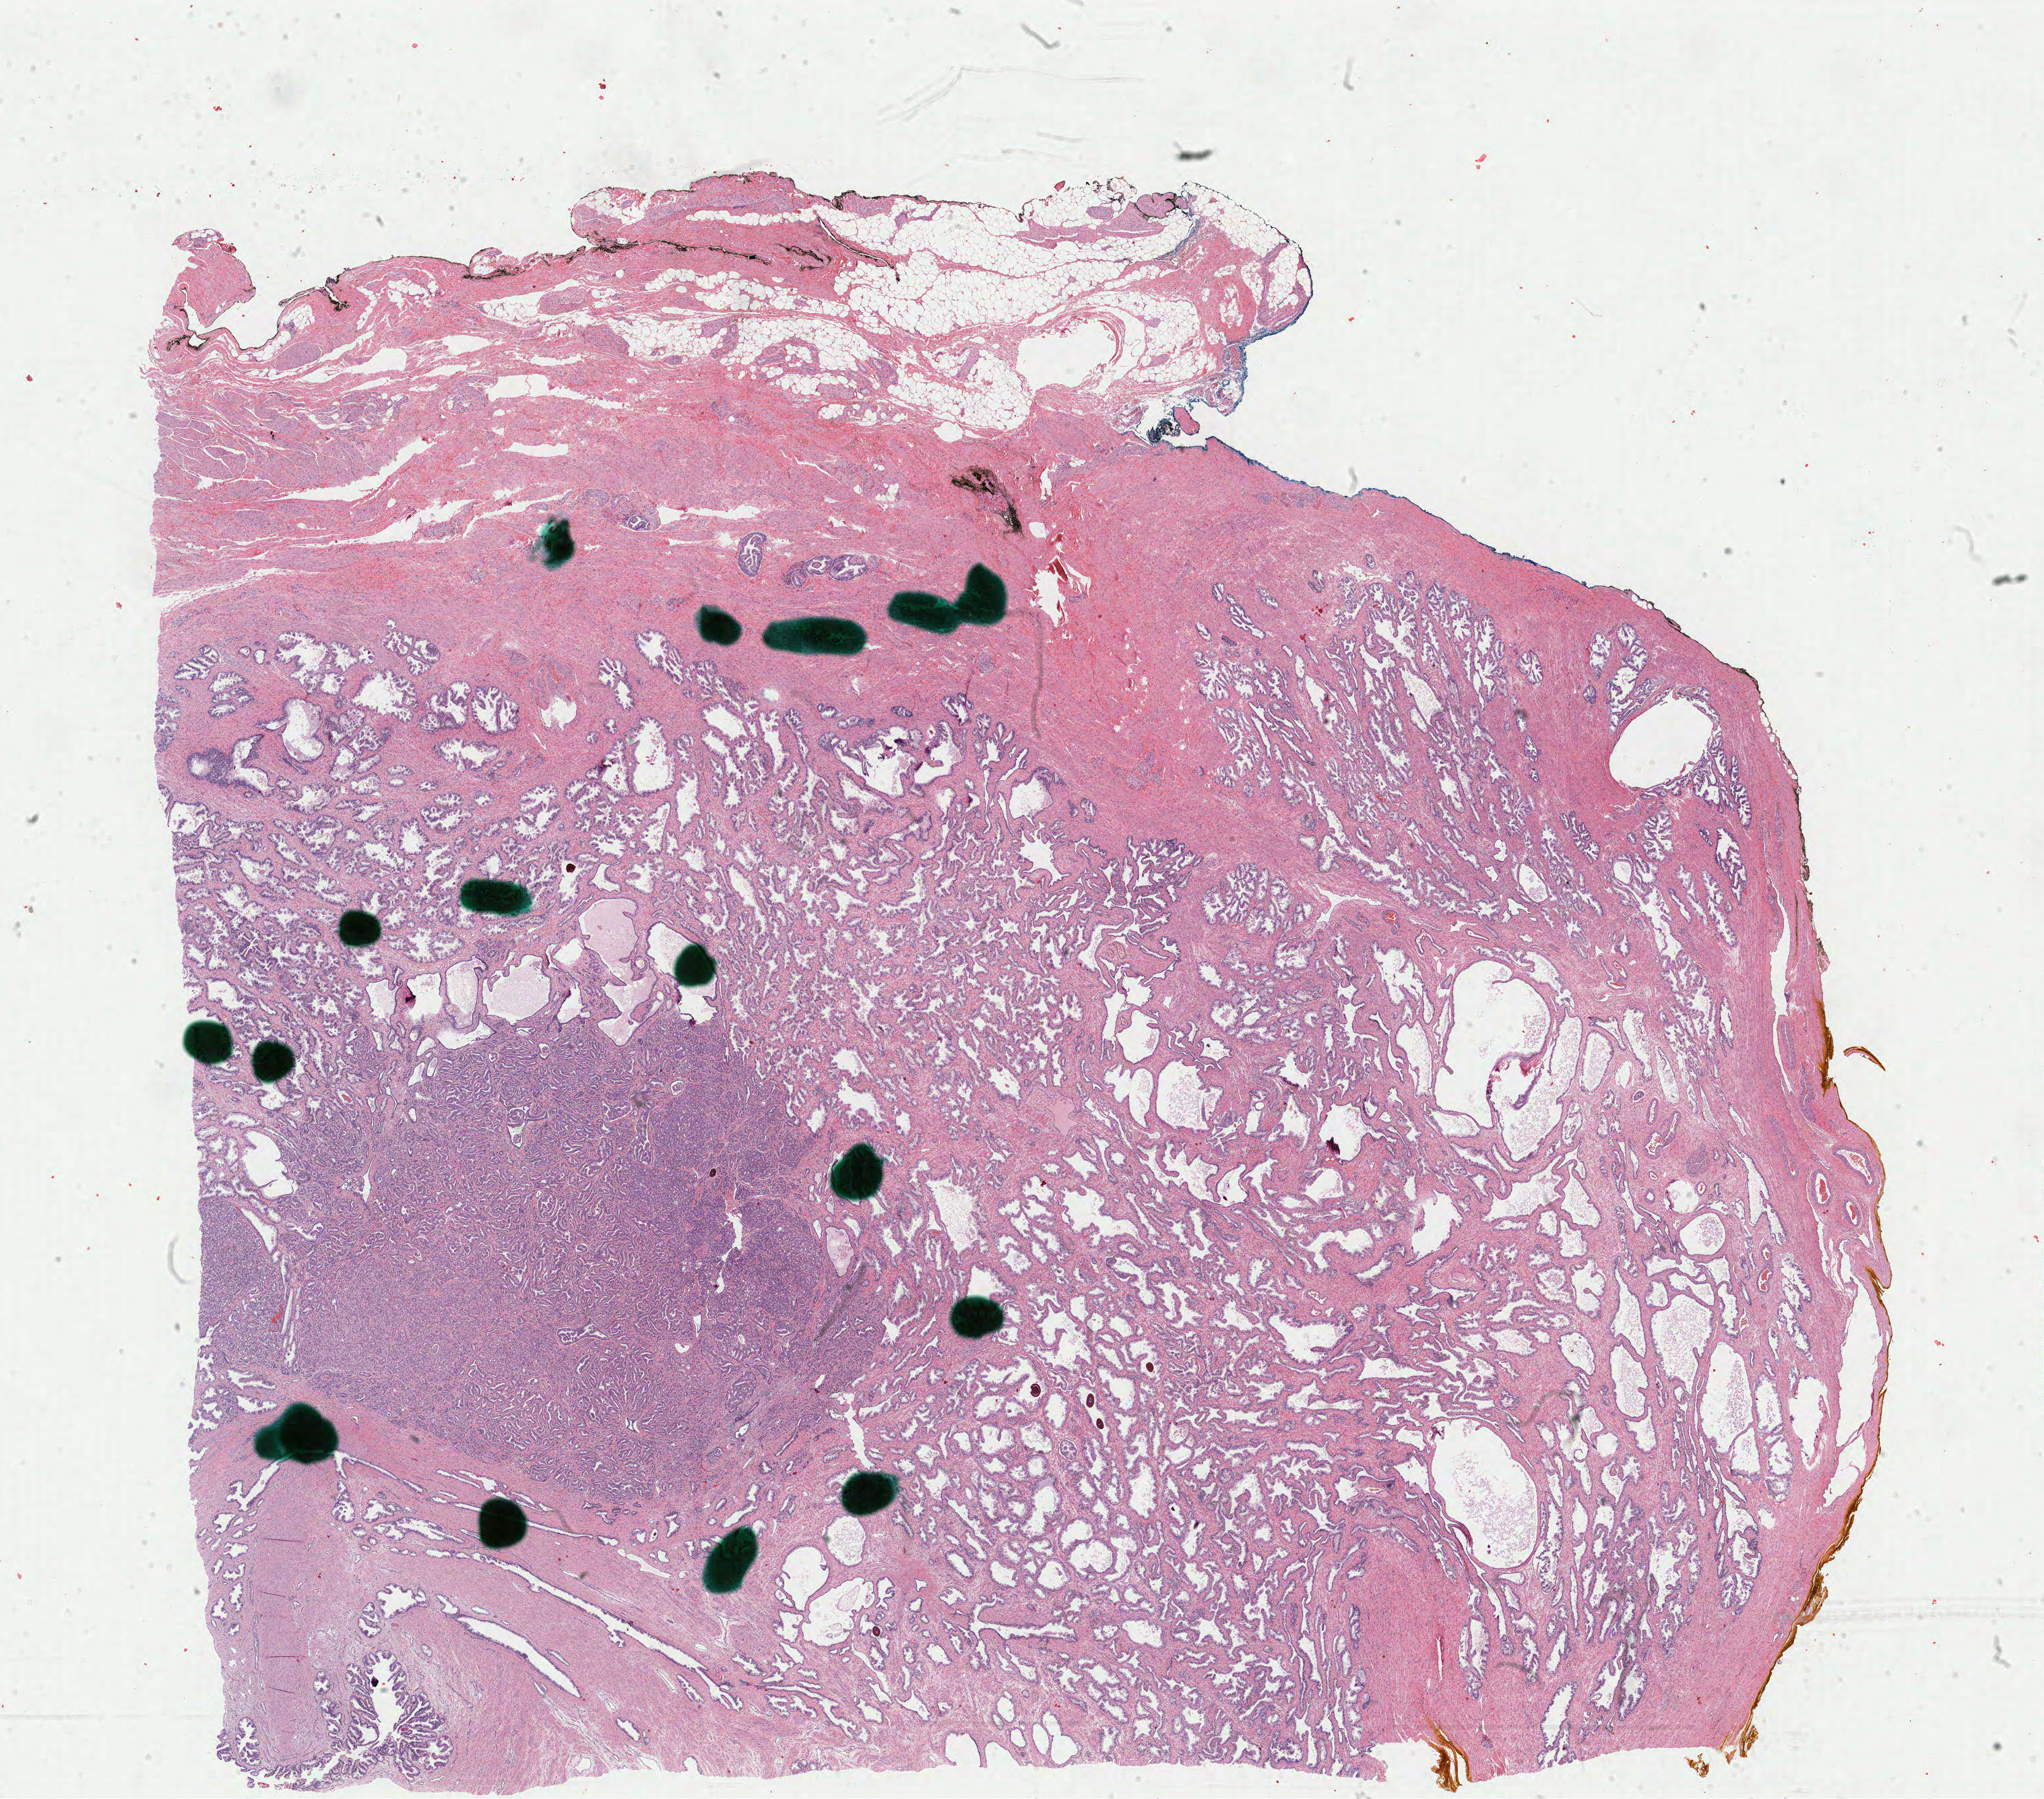
H&E-stained whole-slide image, whole scanned area (about 24.1 x 21.2 mm, slide scanned at 40x) shown as a low-resolution overview. Formalin-fixed paraffin-embedded (FFPE) diagnostic section. Prostate, primary tumour sample. Male patient; age at initial diagnosis 62 years. Gleason score: 7 (4+3).
Histologic diagnosis: Adenocarcinoma, NOS (prostate gland). Lymph nodes positive (case pathology): 0 of 11 examined. Laterality: bilateral.